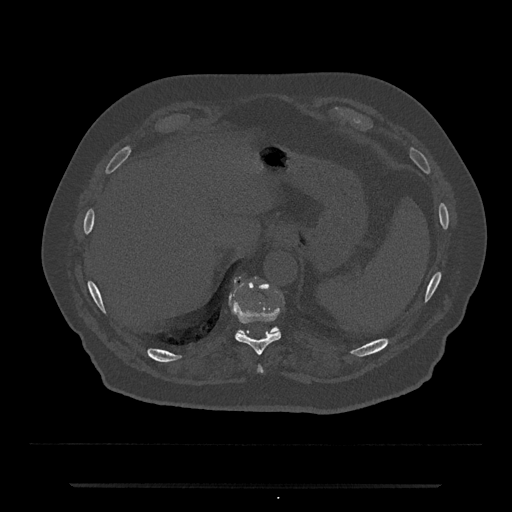
CT including the spine, one axial slice. Position 693 of 797 along the scan axis. Reconstruction kernel Br40s/3. 120 kVp. Bone window (W 1800 / L 400 HU). 512 × 512 image matrix. Male patient, age 80 years. From the clinical record (not read from this slice): primary cancer: prostate; vertebrae with lytic lesions (as recorded): L1, T11.
Structures marked on this image (semi-automatic segmentation, software-assisted and operator-edited):
- T10 vertebra: bounding box <229,278,281,356> (left, top, right, bottom; pixels)
- T11 vertebra: <238,326,280,333>
- T9 vertebra: <258,366,263,372>